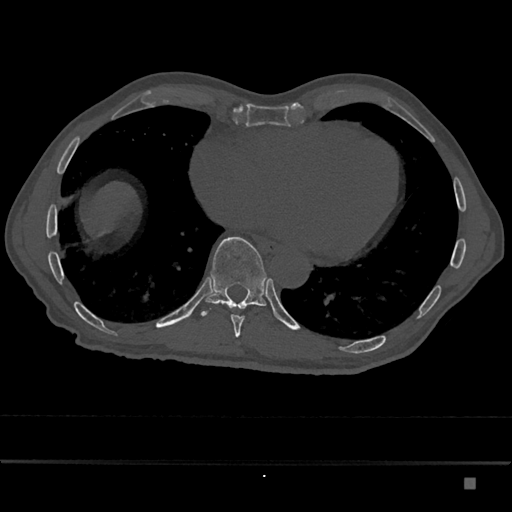
CT including the spine, one axial slice. Position 767 of 797 along the scan axis. Reconstruction kernel Br40s/3. Bone window (W 1800 / L 400 HU). 512 × 512 image matrix, field of view 390 × 390 mm. Patient: male, 72 years. From the clinical record (not read from this slice): primary cancer: prostate.
Structures marked on this image (semi-automatic segmentation, software-assisted and operator-edited):
- T10 vertebra: bounding box (x1, y1, x2, y2) in pixels: (201, 237, 267, 317)
- T9 vertebra: (231, 308, 245, 337)